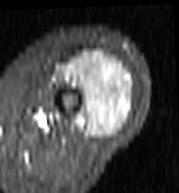
MRI of an extremity soft-tissue mass, one axial slice; slice 45 of 103 in the series (ordered by position); STIR; MR volume resampled by the dataset authors to the PET/CT grid (not the native acquisition matrix); 179 × 193 image matrix, field of view 175 × 188 mm. Female patient. From the clinical record (not read from this slice): histological type: undifferentiated – high grade; grade: high; site of the primary tumour: left thigh.
Structures marked on this image (expert contour drawn on MRI and transferred to this co-registered scan by the dataset authors):
- gross tumour volume including surrounding oedema: bounding box [x1, y1, x2, y2] px = [56, 51, 135, 138]
- gross tumour volume (mass): [70, 51, 133, 138]